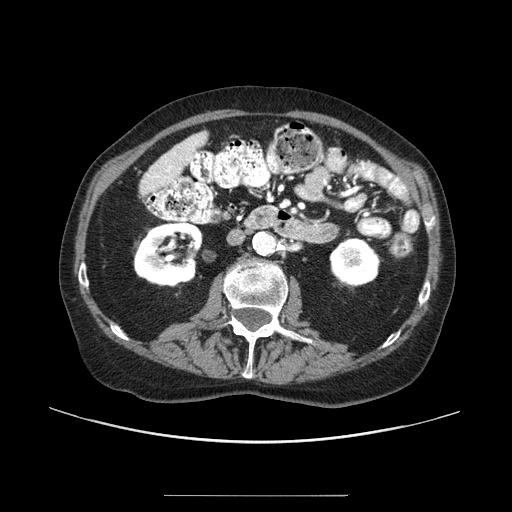
Contrast-enhanced abdominal CT (liver protocol), one axial slice; position 27 of 91 along the scan axis; 100 kVp; one of 2 acquisitions stored at this slice position; soft-tissue window (W 400 / L 40 HU); 2.5 mm slice thickness; 512 × 512 image matrix. From the clinical record (not read from this slice): diagnosis: hepatocellular carcinoma (patient treated with transarterial chemoembolisation; whether this scan precedes or follows treatment is not stated here); TNM stage (as recorded): Stage-I.
Annotated regions visible in this slice (semi-automatic segmentation, software-assisted and operator-edited):
- liver parenchyma outside the tumour (the mass and vessels are separate outlines, so this box may not span the whole liver): bounding box [x1, y1, x2, y2] px = [156, 132, 208, 176]
- liver vessels: [165, 141, 198, 173]